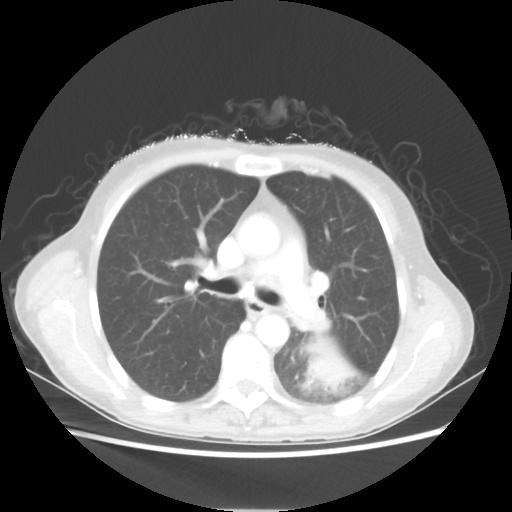
Chest CT, one axial slice; position 34 of 56 along the scan axis; reconstruction kernel STANDARD; lung window (W 1500 / L -600 HU); 5 mm slice thickness; 512 × 512 image matrix. Patient: female, 53 years. From the clinical record (not read from this slice): clinical TNM (as recorded): T3 N0 M0.
Annotated regions visible in this slice (rectangle marked by the reading radiologist):
- lung tumour (recorded histology: adenocarcinoma): box from (x=303, y=338) to (x=355, y=392) px